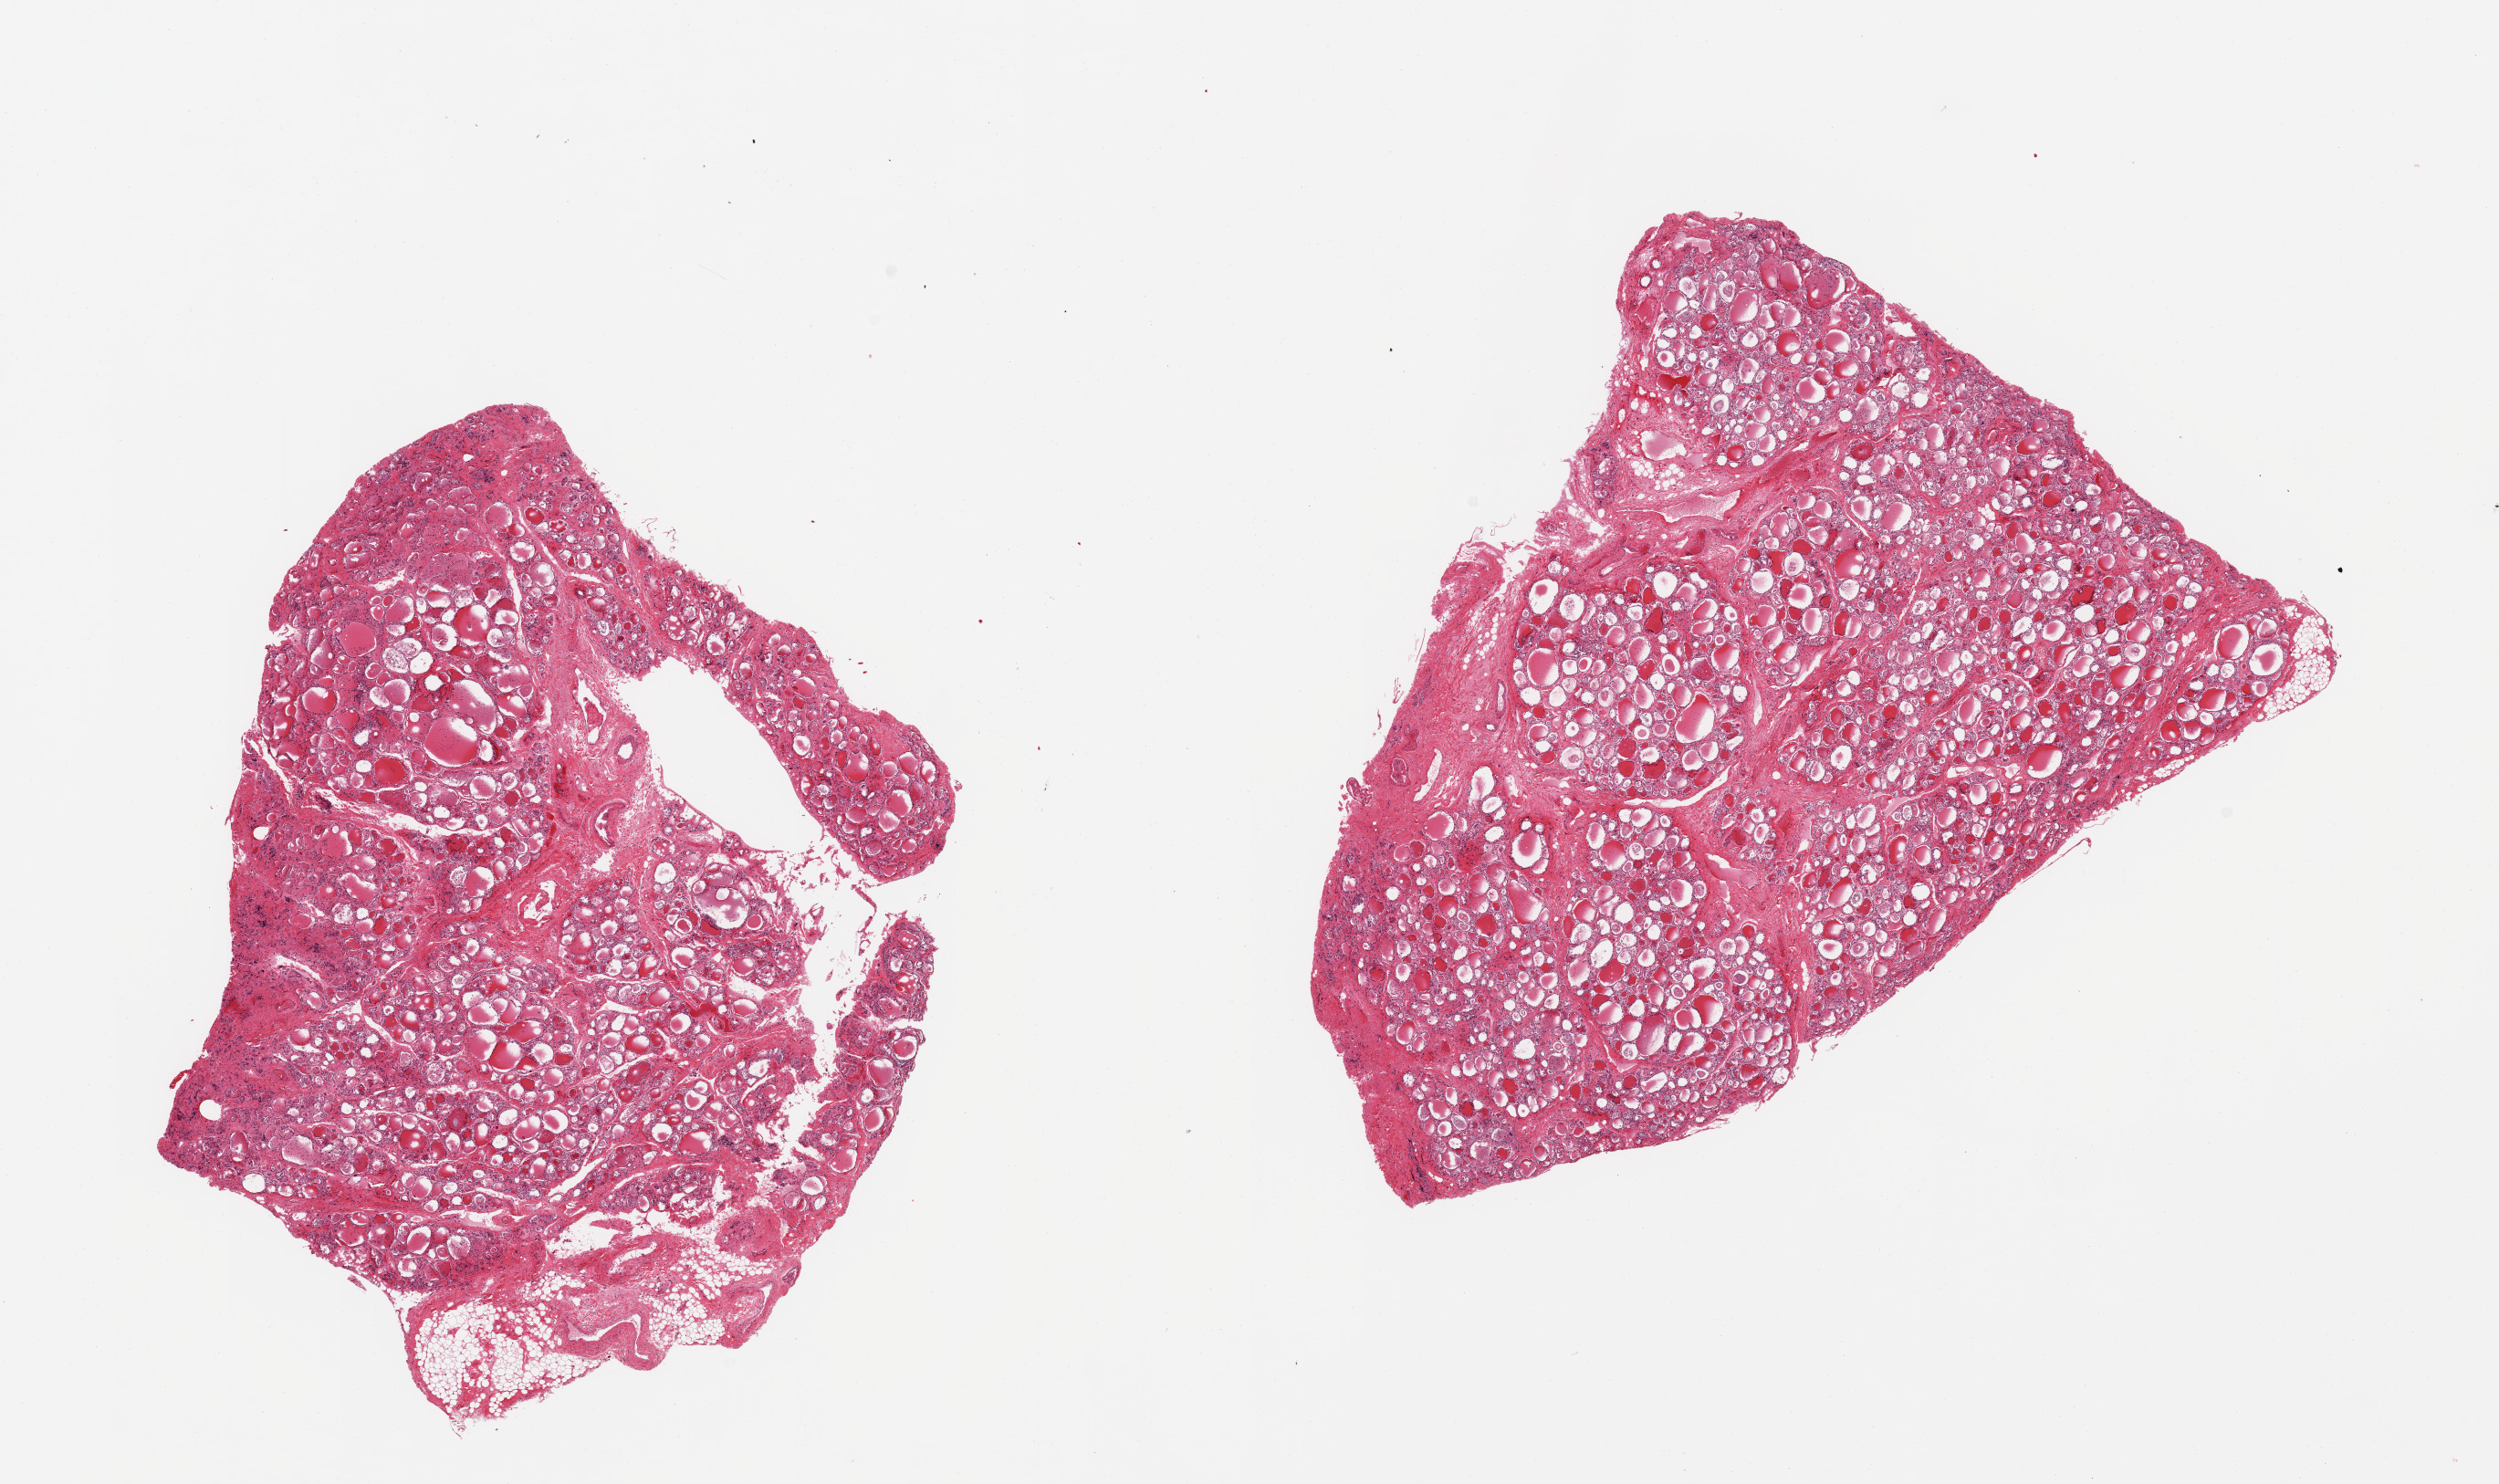
H&E whole-slide image — shown as a low-resolution overview of the whole scanned area (about 21.7 x 12.9 mm, slide scanned at 20x). PAXgene-fixed paraffin-embedded (PFPE) section. Sampled site (target tissue): thyroid. Tissue donor sample.
• reviewer comment on this tissue sample: 2 pieces; some foci are moderately autolyzed